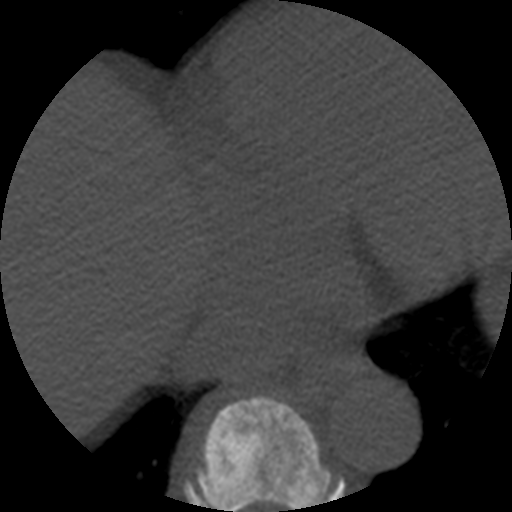
CT including the spine, one axial slice. Position 306 of 508 along the scan axis. 120 kVp. Bone window (W 1800 / L 400 HU). 512 × 512 image matrix, field of view 160 × 160 mm. Patient age 57 years. From the clinical record (not read from this slice): primary cancer: prostate.
Annotated regions visible in this slice (semi-automatically segmented with operator editing):
- T8 vertebra: box from (x=197, y=395) to (x=332, y=512) px